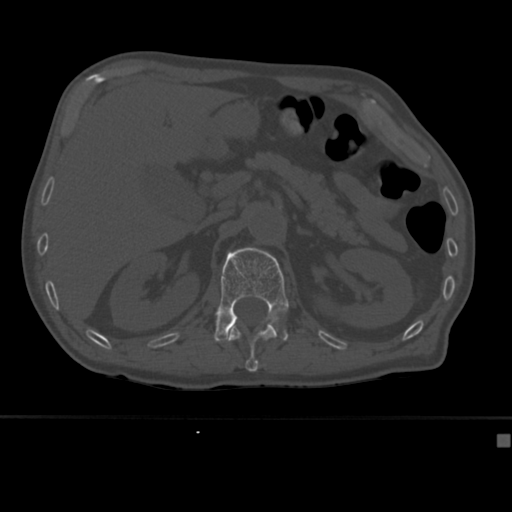
CT including the spine, one axial slice; position 176 of 430 along the scan axis; bone window (W 1800 / L 400 HU); 1.5 mm slice thickness; 512 × 512 image matrix, field of view 337 × 337 mm. Patient: male, 64 years. From the clinical record (not read from this slice): primary cancer: uterus; vertebrae with lytic lesions (as recorded): T1, T4, T5, T7, L5.
Structures marked on this image (semi-automatic segmentation, software-assisted and operator-edited):
- L1 vertebra: bounding box [x1, y1, x2, y2] px = [214, 247, 289, 342]
- T12 vertebra: [229, 320, 277, 372]